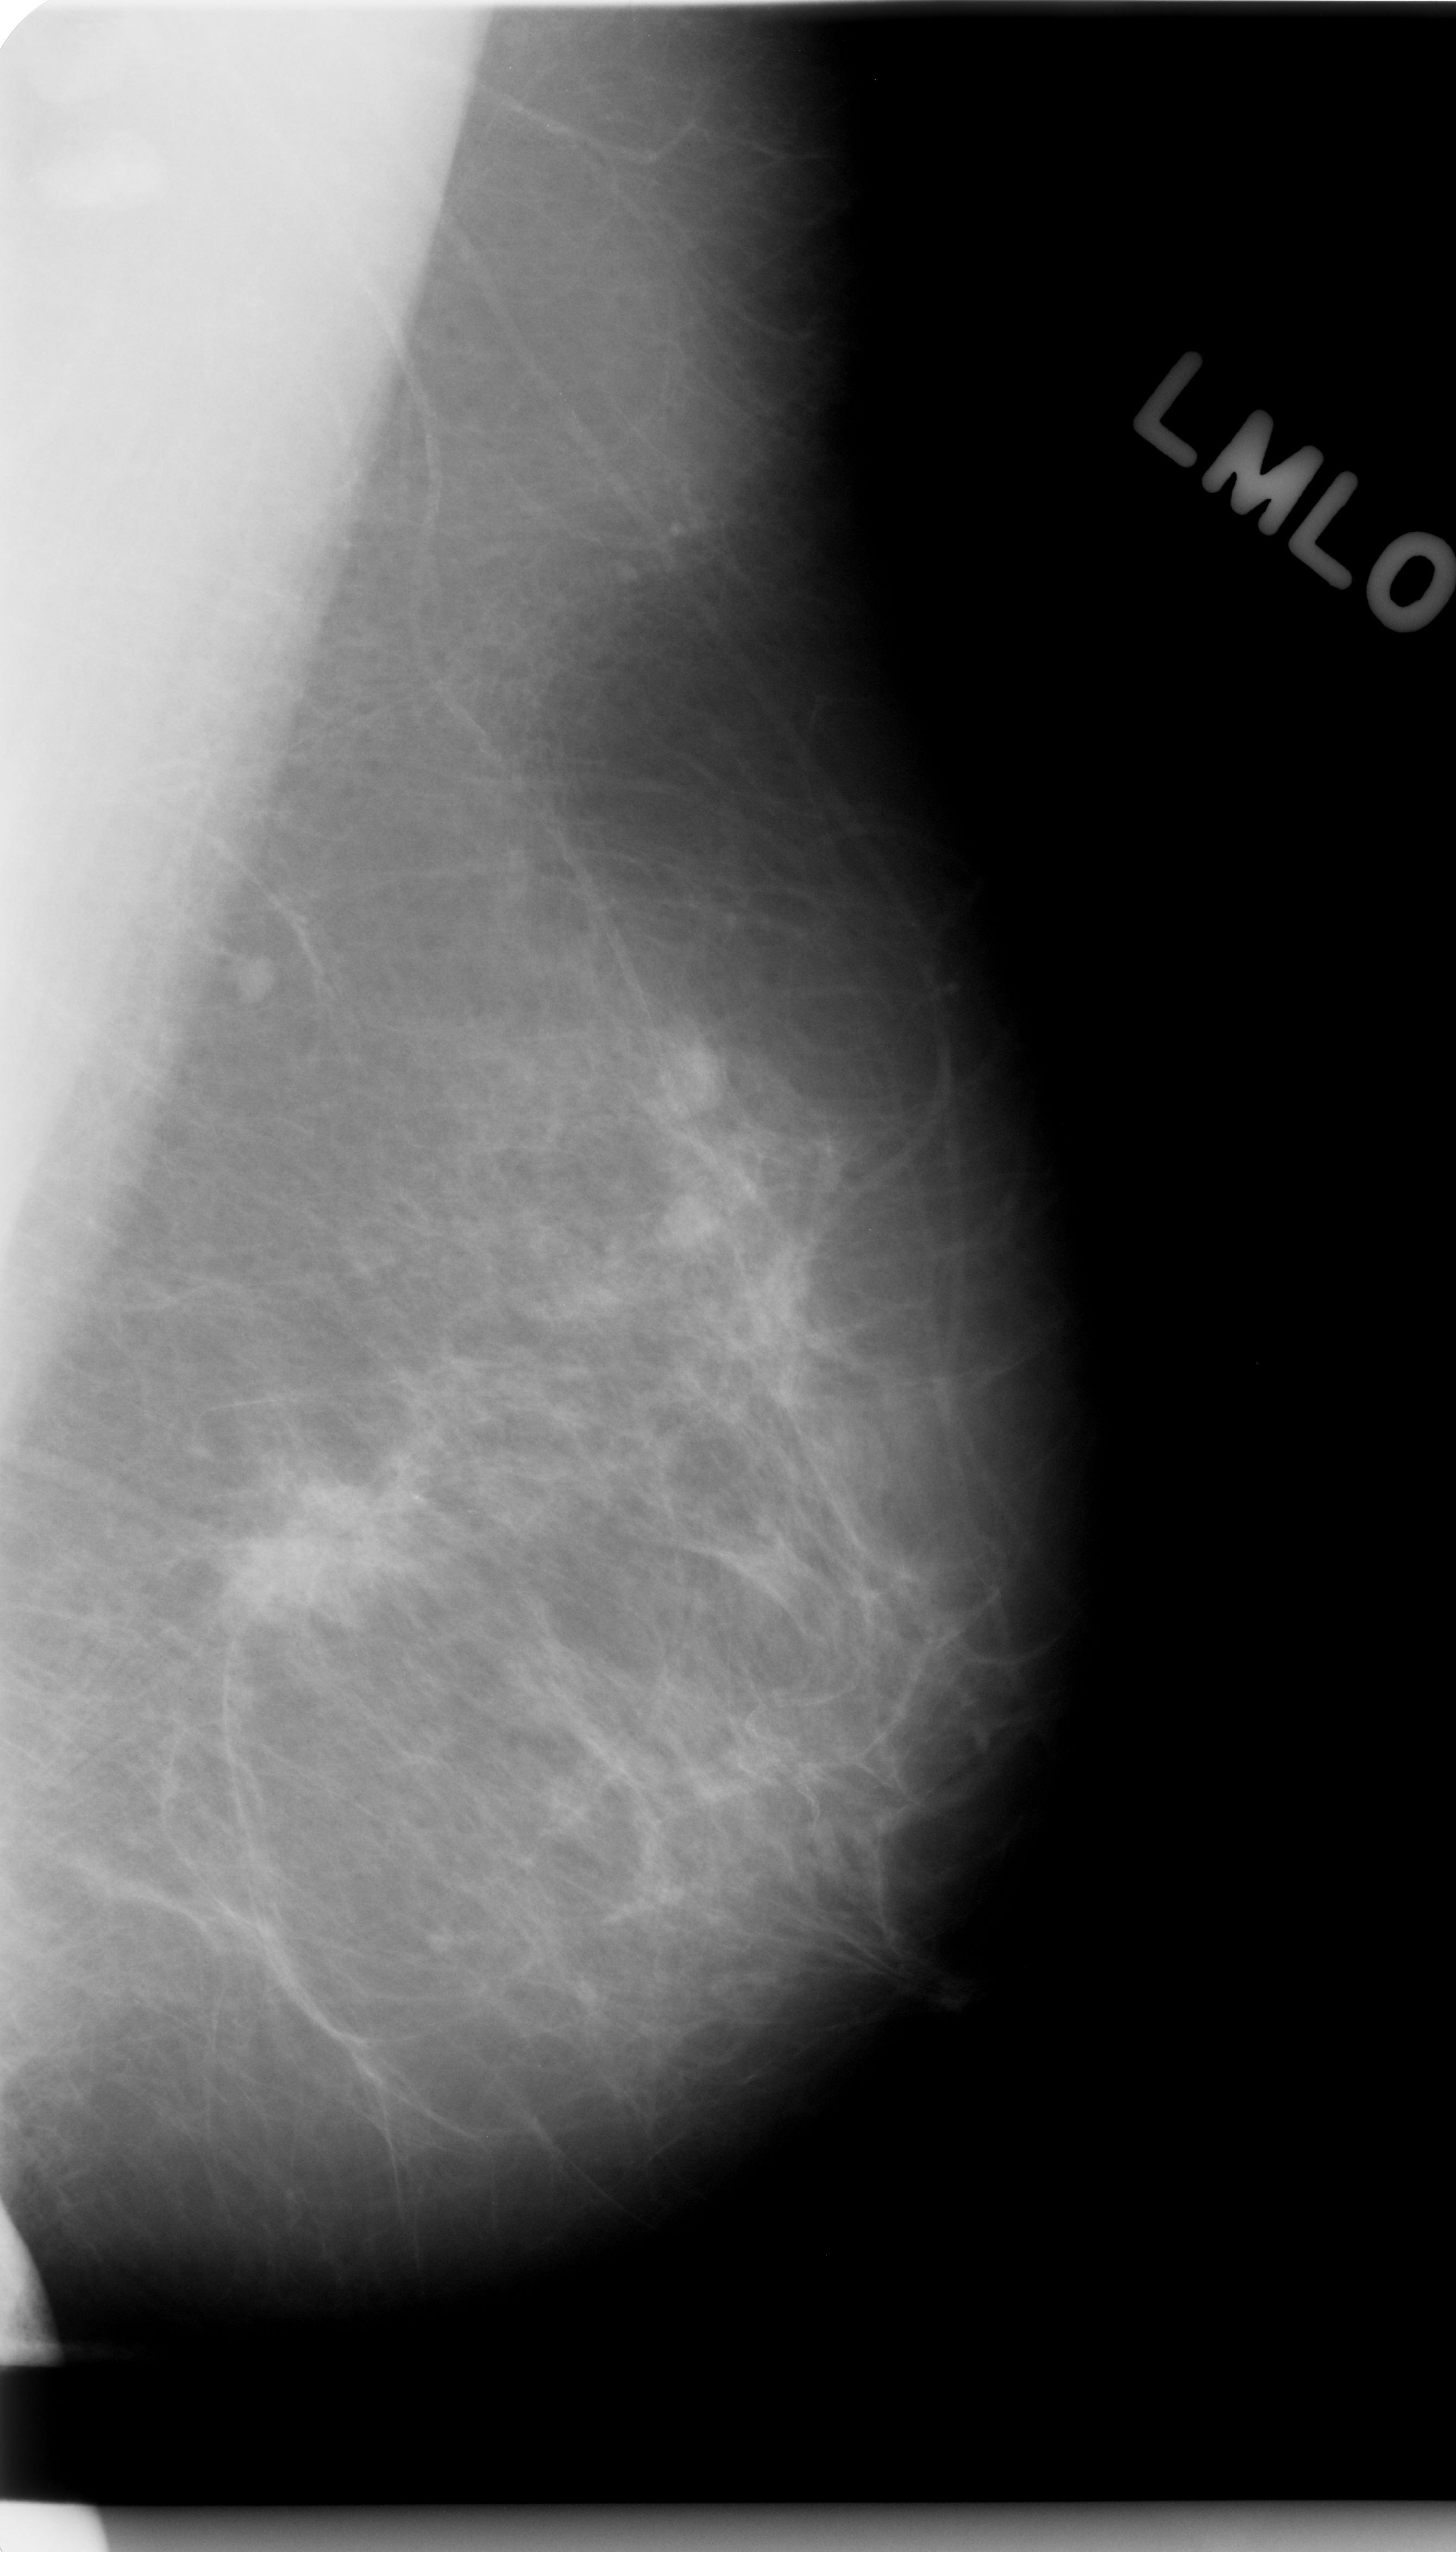
Digitized screen-film mammogram; left breast; mediolateral oblique (MLO) view; 1456 × 2552 image matrix.
Marked abnormalities (boxes around the expert regions of interest):
- mass, shape irregular, margins spiculated; BI-RADS assessment category 5; pathology (as recorded): malignant: bounding box [x1, y1, x2, y2] px = [203, 1451, 427, 1642]